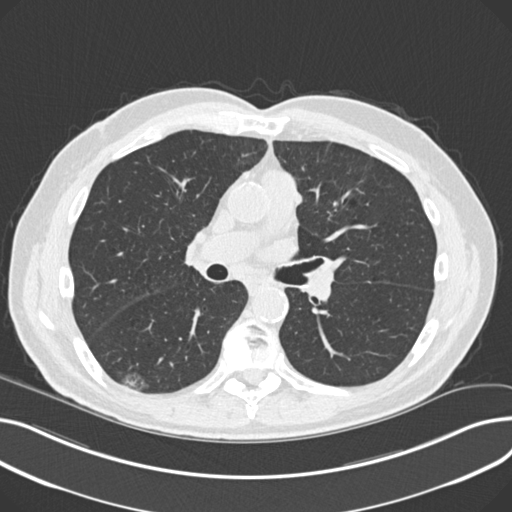
Low-dose screening chest CT, one axial slice. Position 123 of 230 along the scan axis. Reconstruction kernel B30f. 120 kVp. Lung window (W 1500 / L -600 HU). 2 mm slice thickness. 512 × 512 image matrix, field of view 372 × 372 mm.
Structures marked on this image (expert manual segmentation):
- lesion 1 (nodule, lower lobe of right lung): bounding box <120,373,146,391> (left, top, right, bottom; pixels)